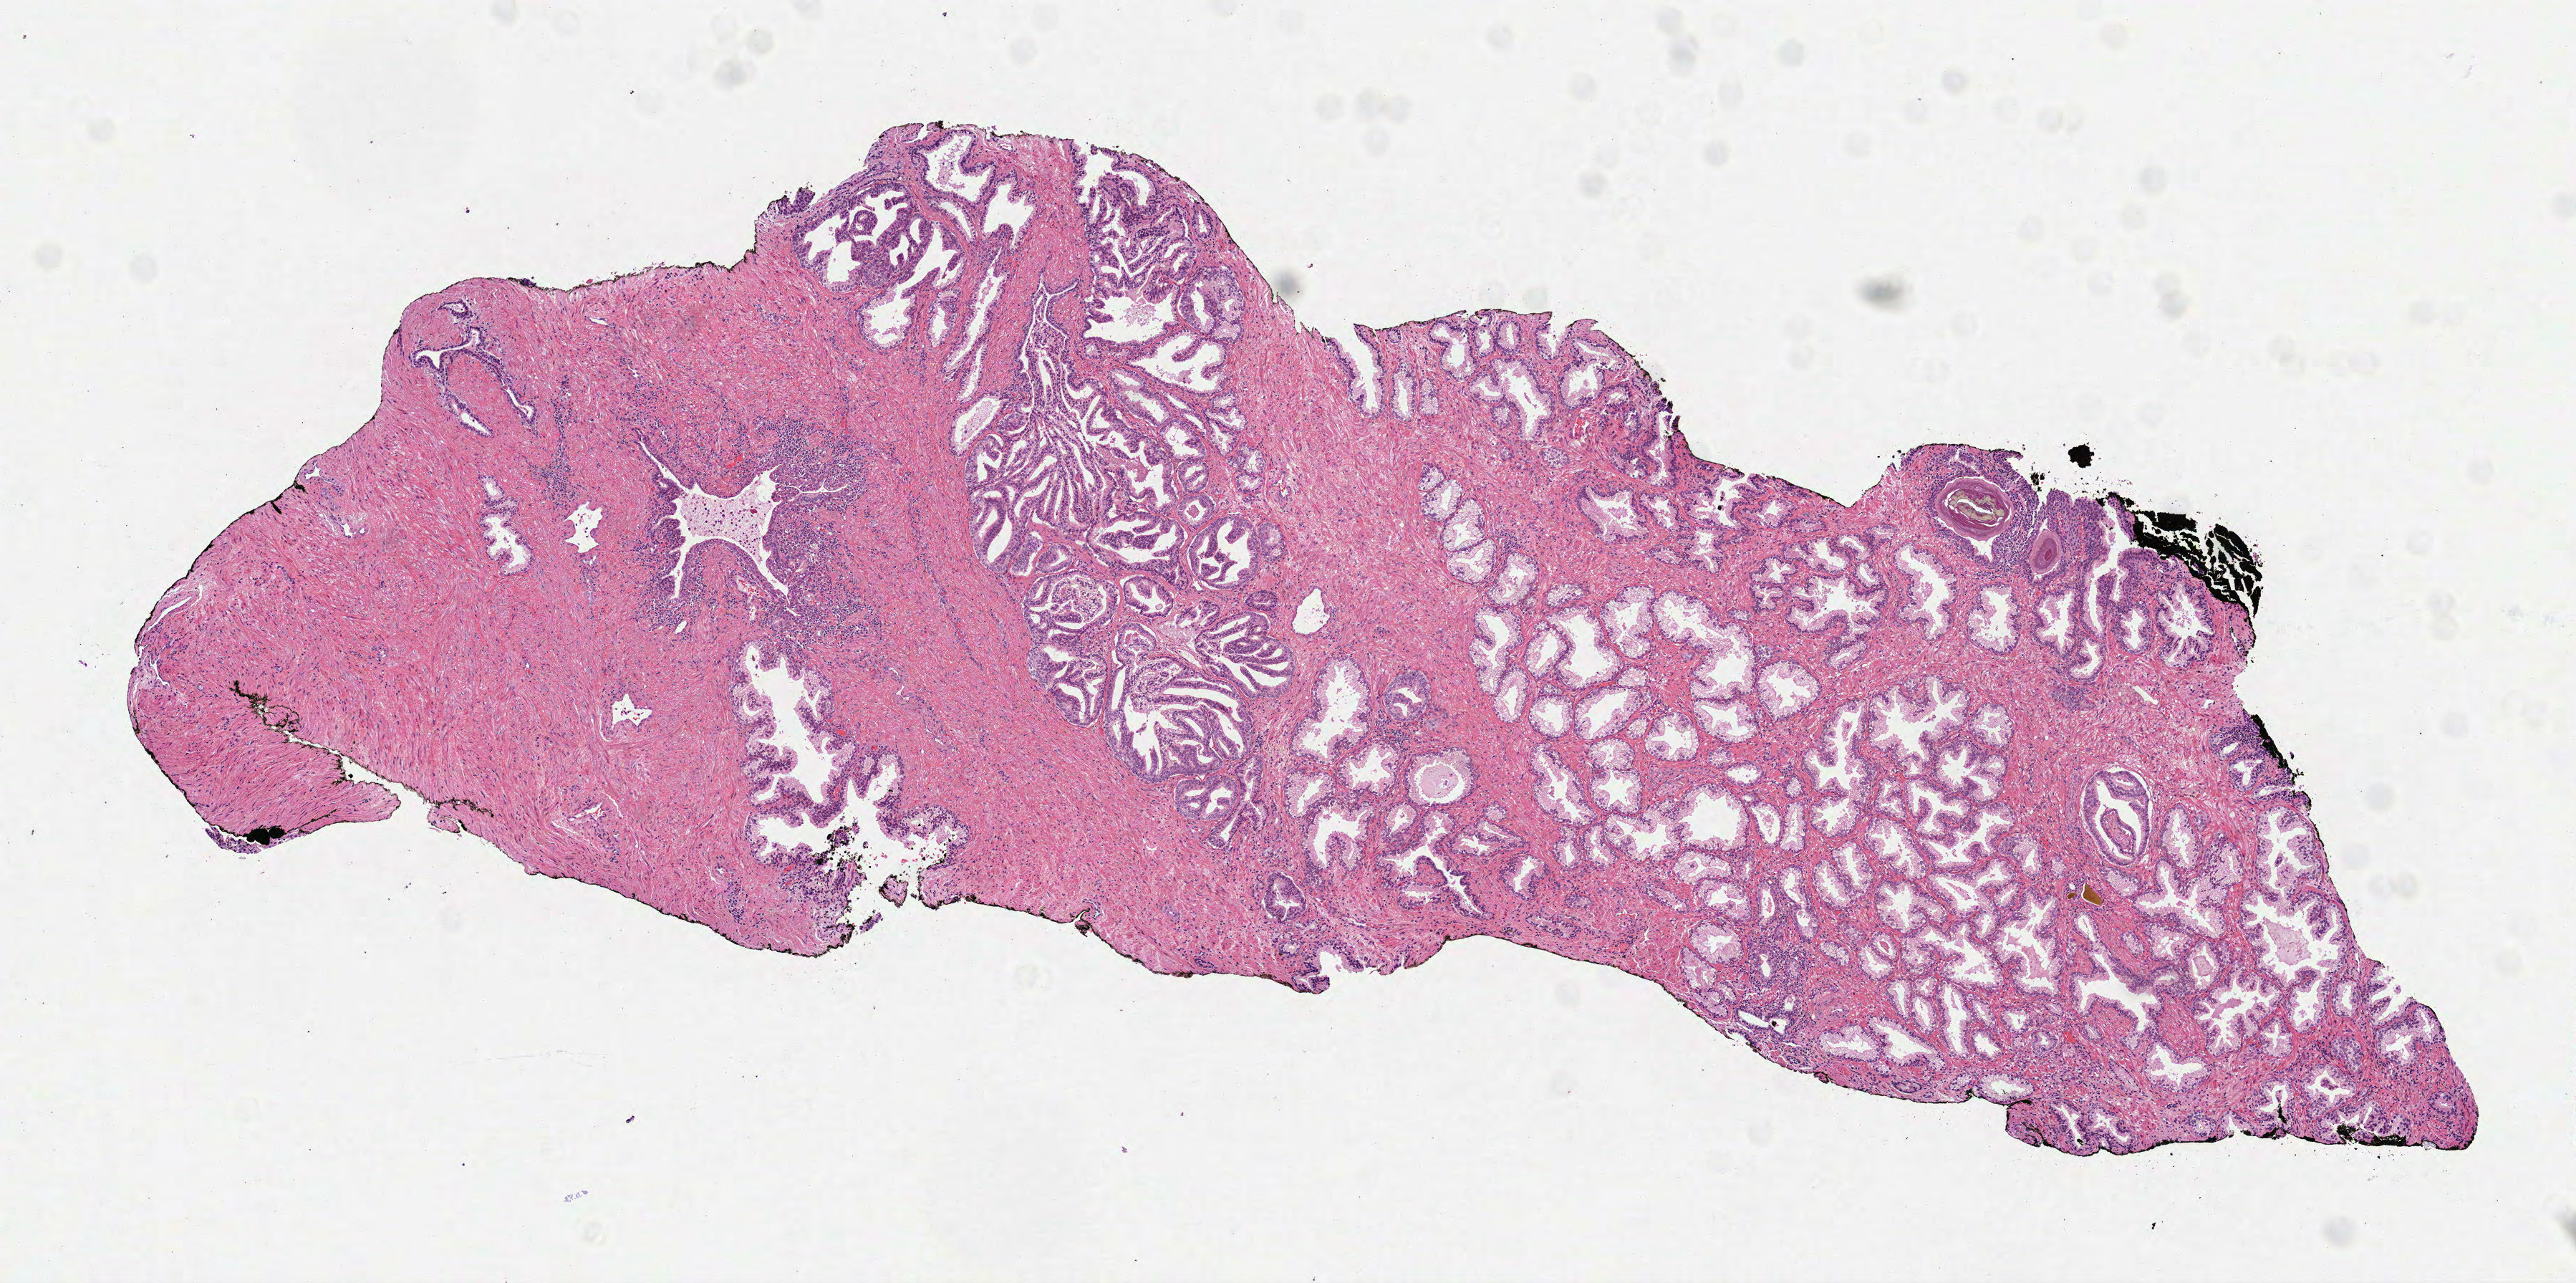
Digitized Hematoxylin and eosin (H&E) stained tissue section (whole slide), low-resolution overview of the scanned area, about 7.3 x 3.6 mm; formalin-fixed paraffin-embedded (FFPE) diagnostic section; prostate, primary tumour sample. Patient: male, age at initial diagnosis 66 years. Gleason score: 7 (3+4).
• histologic diagnosis: Acinar cell carcinoma (prostate gland)
• laterality: bilateral